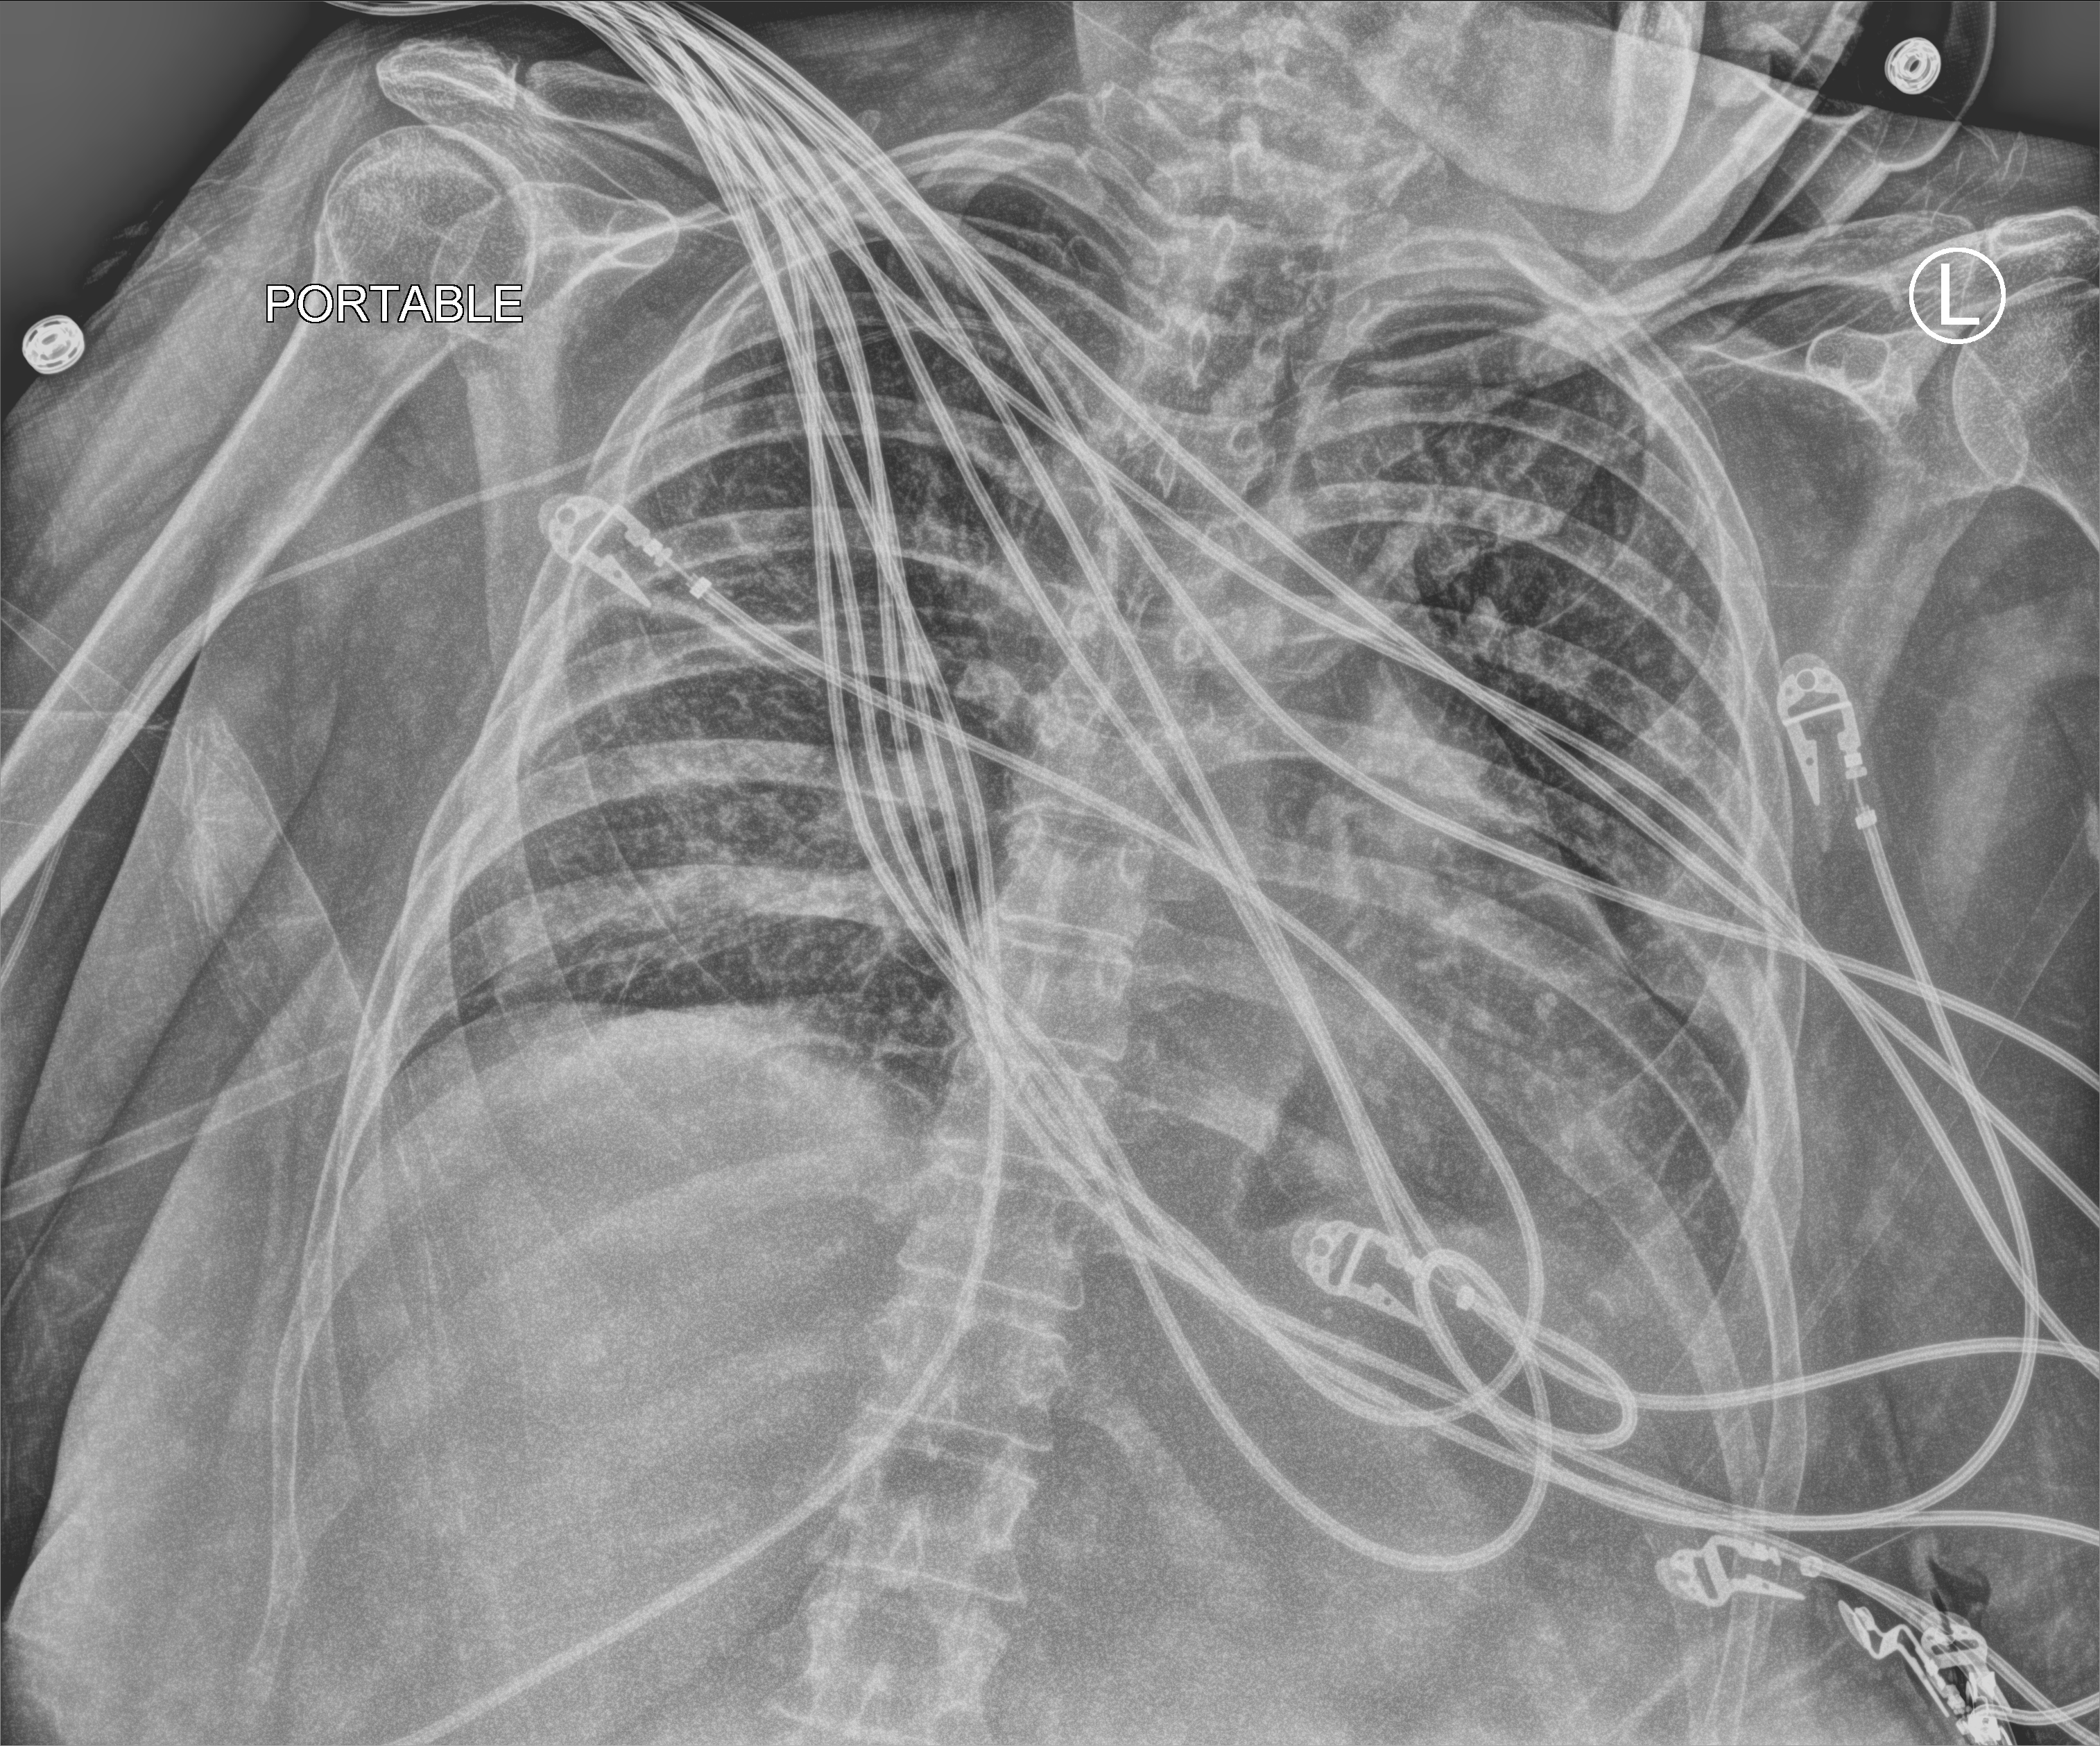
Portable chest radiograph, anteroposterior (AP) projection. Female patient hospitalised with COVID-19, age 60–74 years.
From the hospital-stay record, not from the radiograph (when in the stay this image was taken is not recorded):
- admitted to intensive care during this hospital stay: yes
- mechanically ventilated during this hospital stay: yes